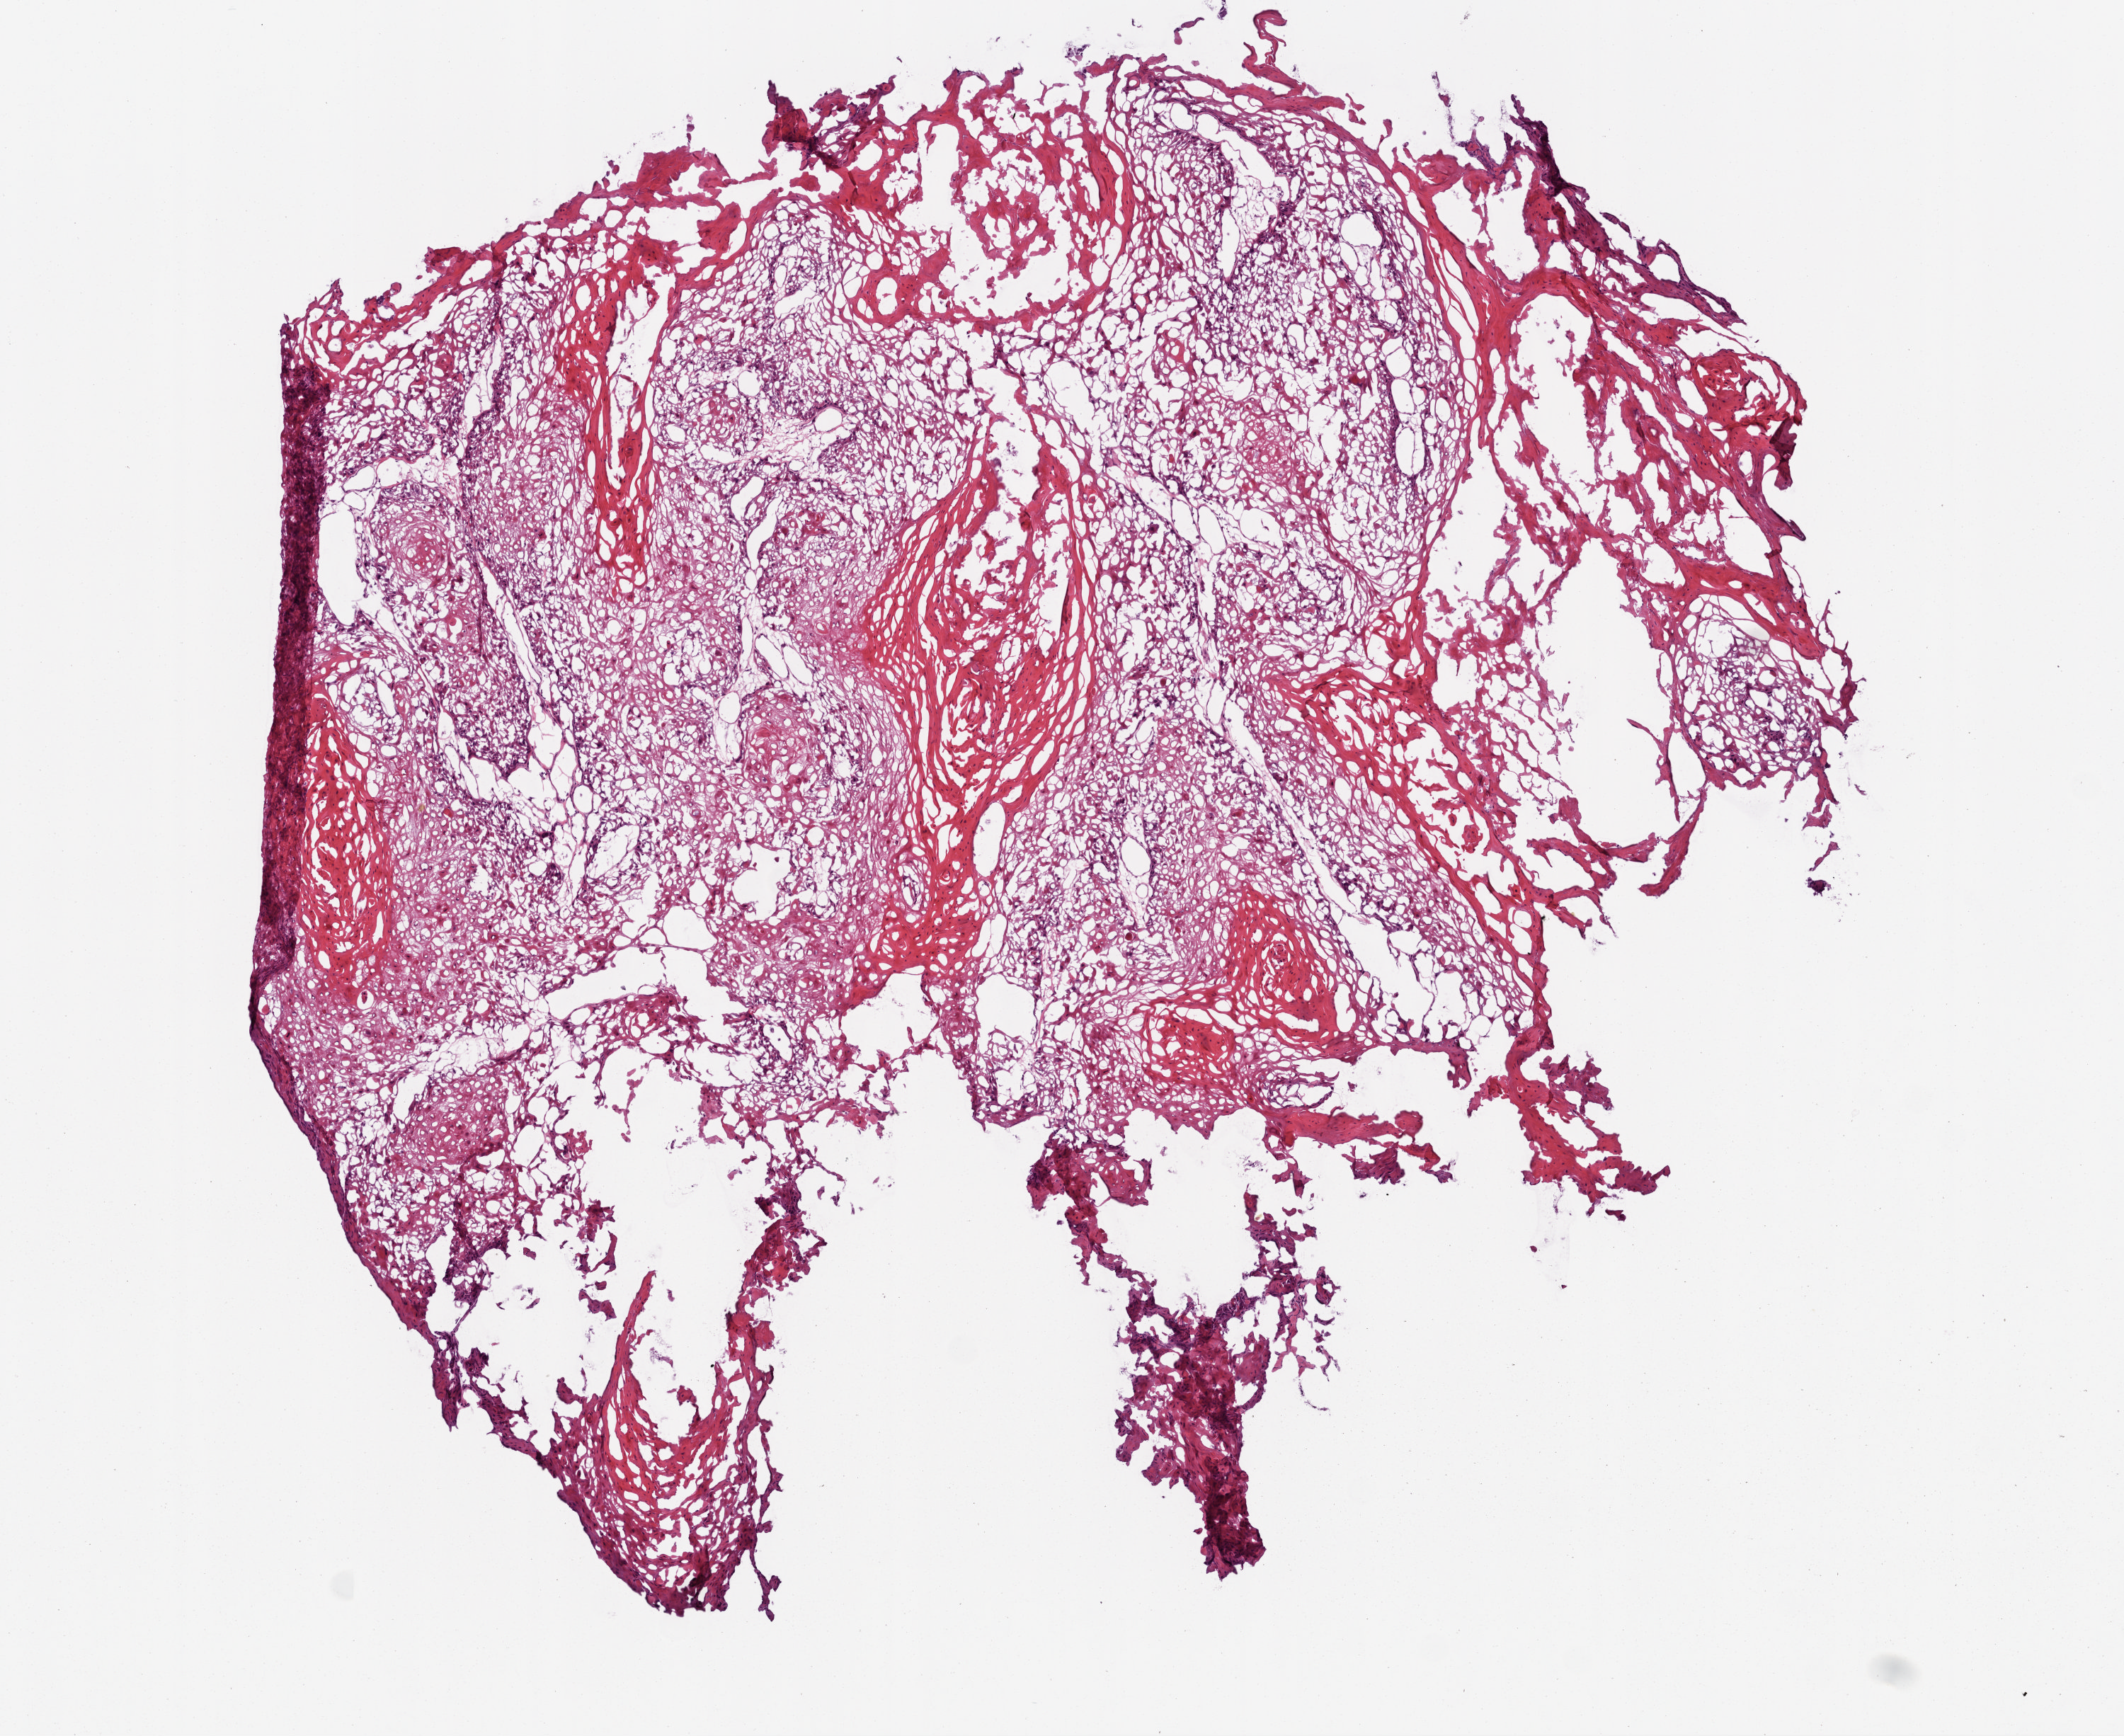
H&E-stained whole-slide image, low-resolution overview of the scanned area, about 6.0 x 4.9 mm. Frozen section. Primary tumour sample from the head and neck. Male patient; age at initial diagnosis 38 years. Histologic grade: G2 (moderately differentiated). Slide review estimates, as recorded: tumour cells 98%, tumour nuclei 90%, normal cells 0%, stromal cells 2%, necrosis 0%.
- lymph nodes positive (case pathology): 1 of 9 examined
- laterality: right
- AJCC pathologic stage: IVB (6th edition)
- histologic diagnosis: Squamous cell carcinoma, NOS